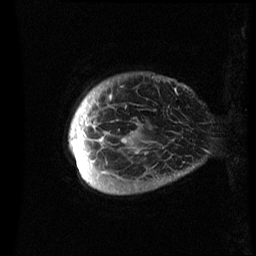
Breast MRI (dynamic contrast-enhanced), one sagittal slice; position 1 of 60 along the scan axis; dynamic contrast-enhanced series, image 2 of 3 at this slice position (ordered by acquisition); 1.5 T; TE 4.2 ms, TR 8.4 ms; 256 × 256 image matrix. Female patient, age 48 years.
Annotated regions visible in this slice (semi-automatically segmented with operator editing):
- analysis volume of interest (the breast-tissue region the enhancement analysis was run in; not a lesion): bounding box (x1, y1, x2, y2) in pixels: (69, 80, 194, 194)
- tumour enhancement mask (voxels above the 70 % enhancement threshold inside the analysis volume of interest): (69, 100, 126, 179)